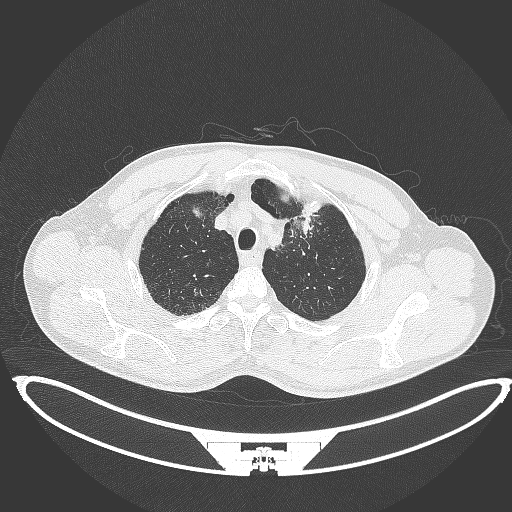
Chest CT, one axial slice; lung window (W 1500 / L -600 HU); 1 mm slice thickness; 512 × 512 image matrix, field of view 457 × 457 mm. Patient: male, 60 years. Case-level facts recorded for this patient, not image findings: clinical TNM (as recorded): T2a N0 M0; histopathological grade: G1-G2.
Outlined on this slice (bounding box drawn by a radiologist):
- lung tumour (recorded histology: squamous cell carcinoma): bounding box (x1, y1, x2, y2) in pixels: (284, 211, 314, 239)